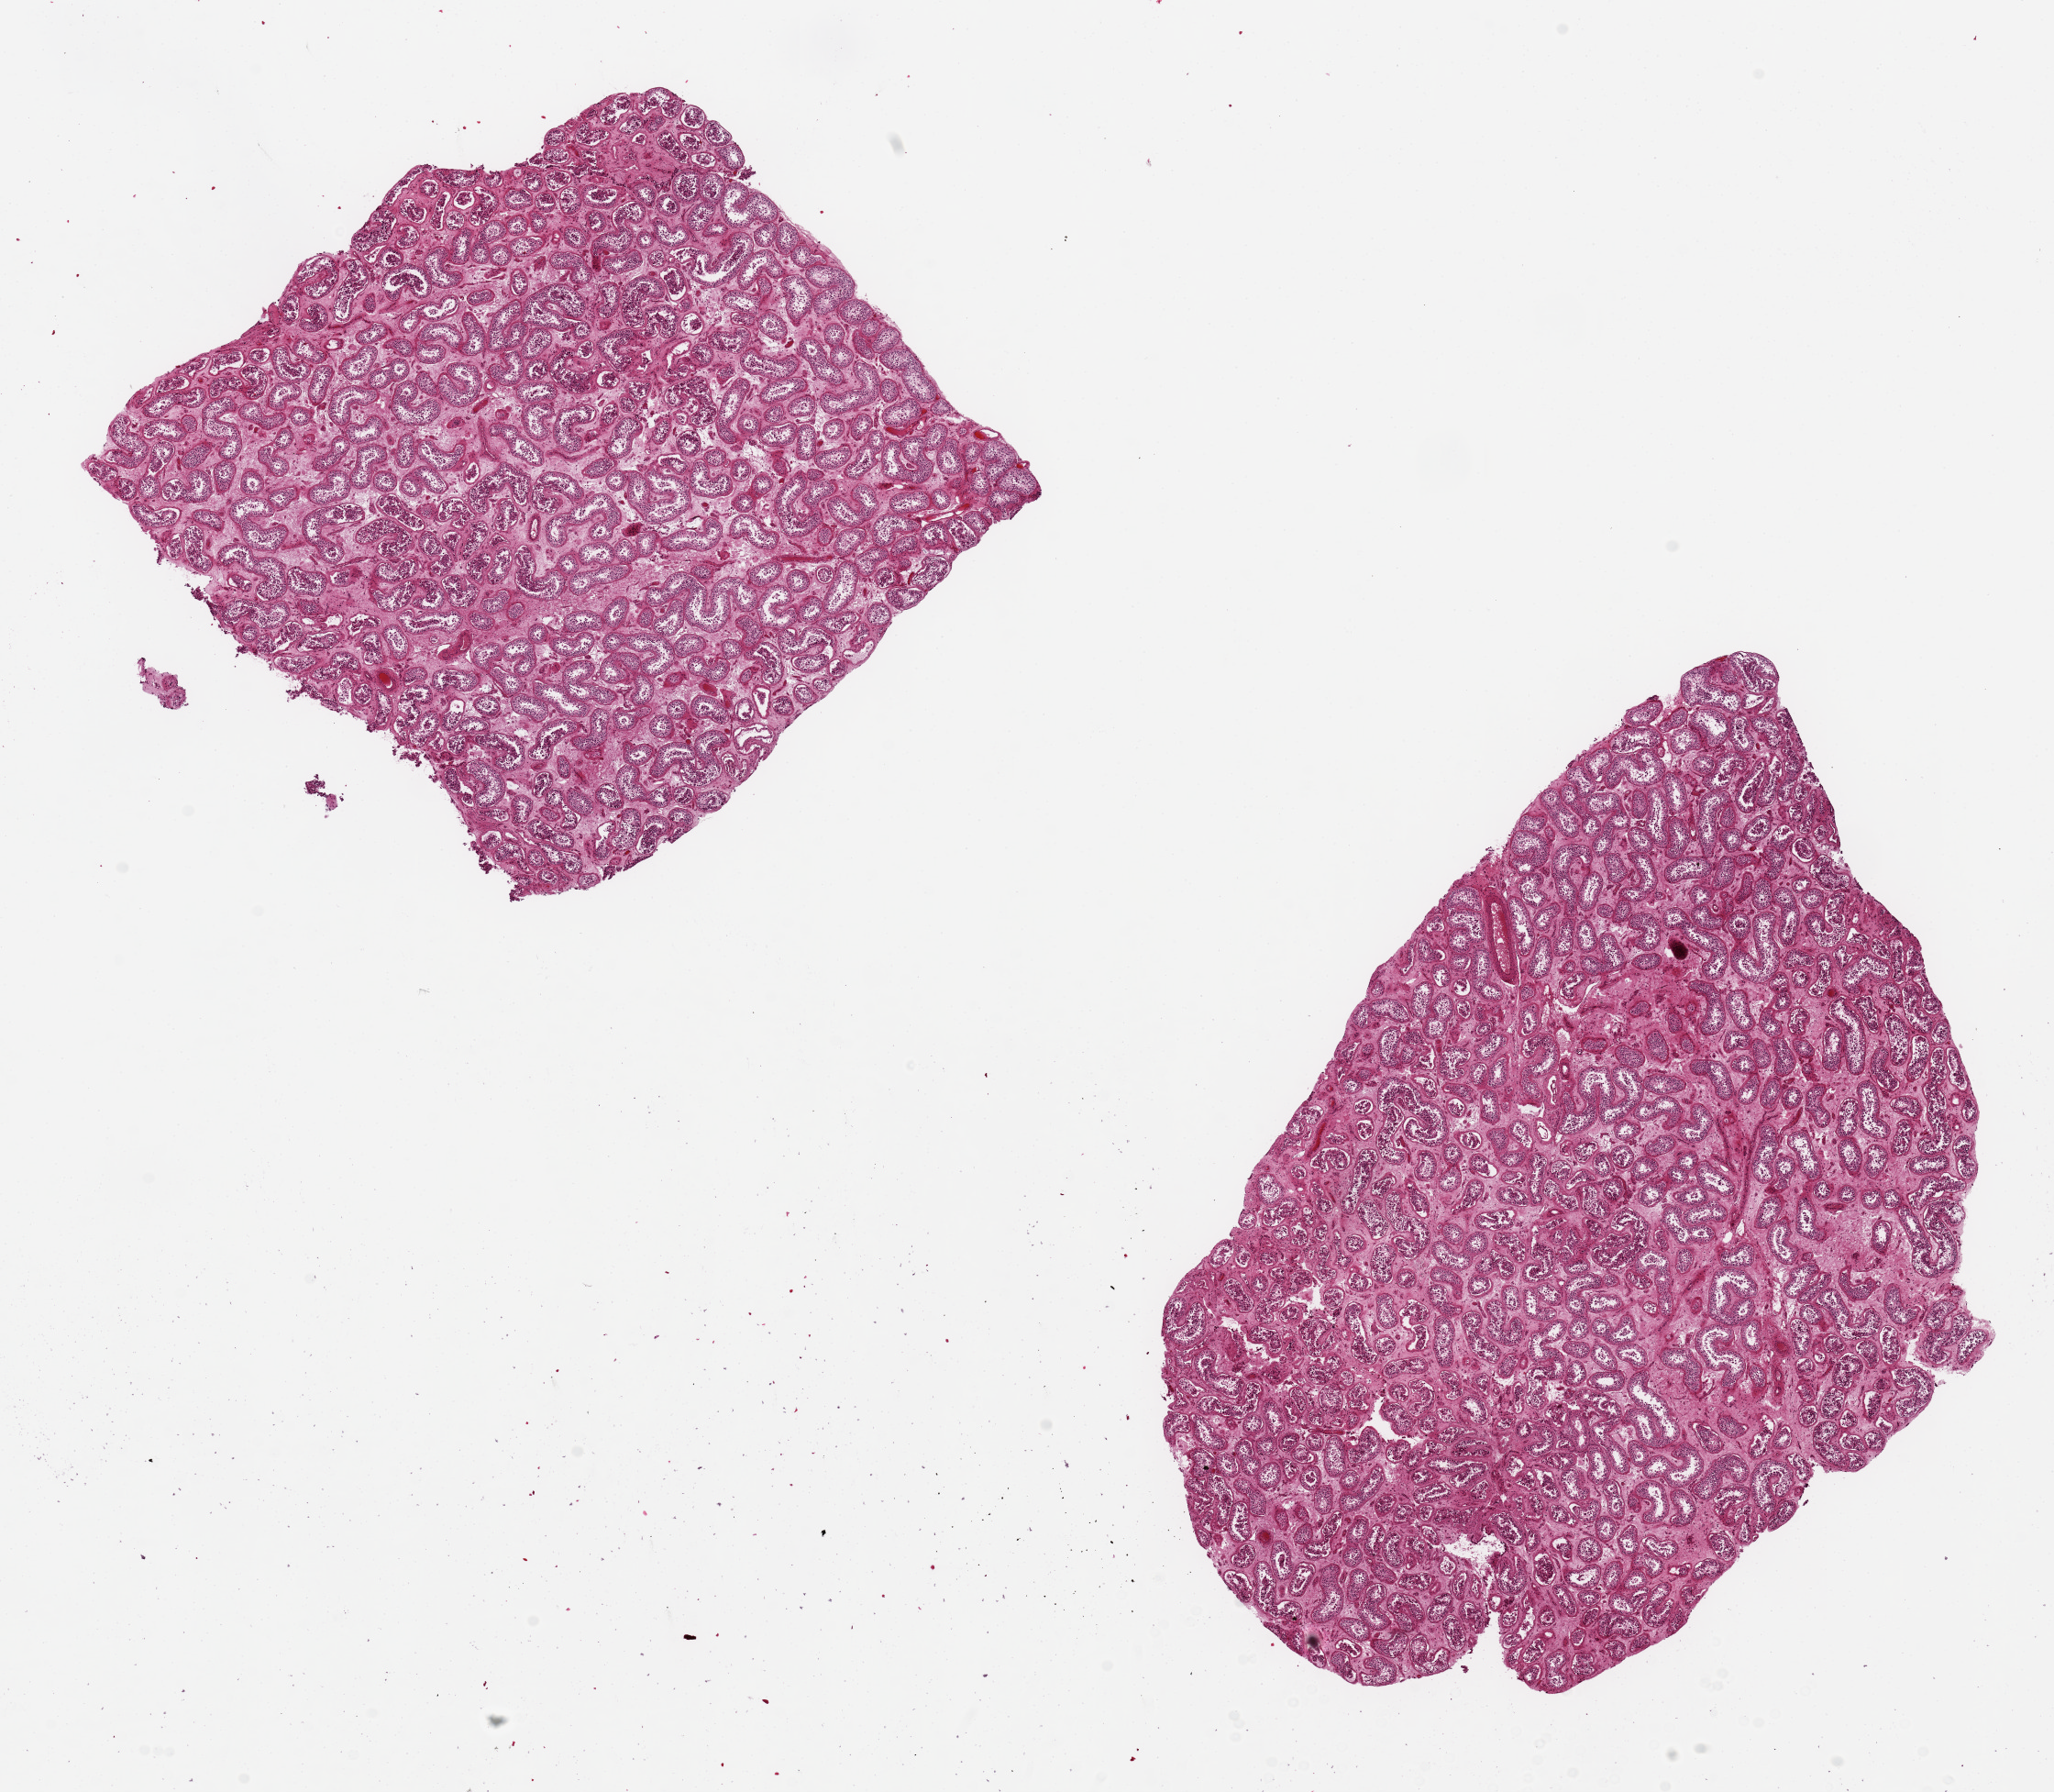
Whole-slide image, haematoxylin and eosin stain, brightfield — shown as a low-resolution overview of the whole scanned area (about 17.7 x 15.5 mm, slide scanned at 20x), PAXgene-fixed paraffin-embedded (PFPE) section, sampled site (target tissue): testis, donor tissue sample. Donor sex: male.
Reviewer comment on this tissue sample: 1 pieces 8x6 & 6x5 mm; reduced spermatogenesis.